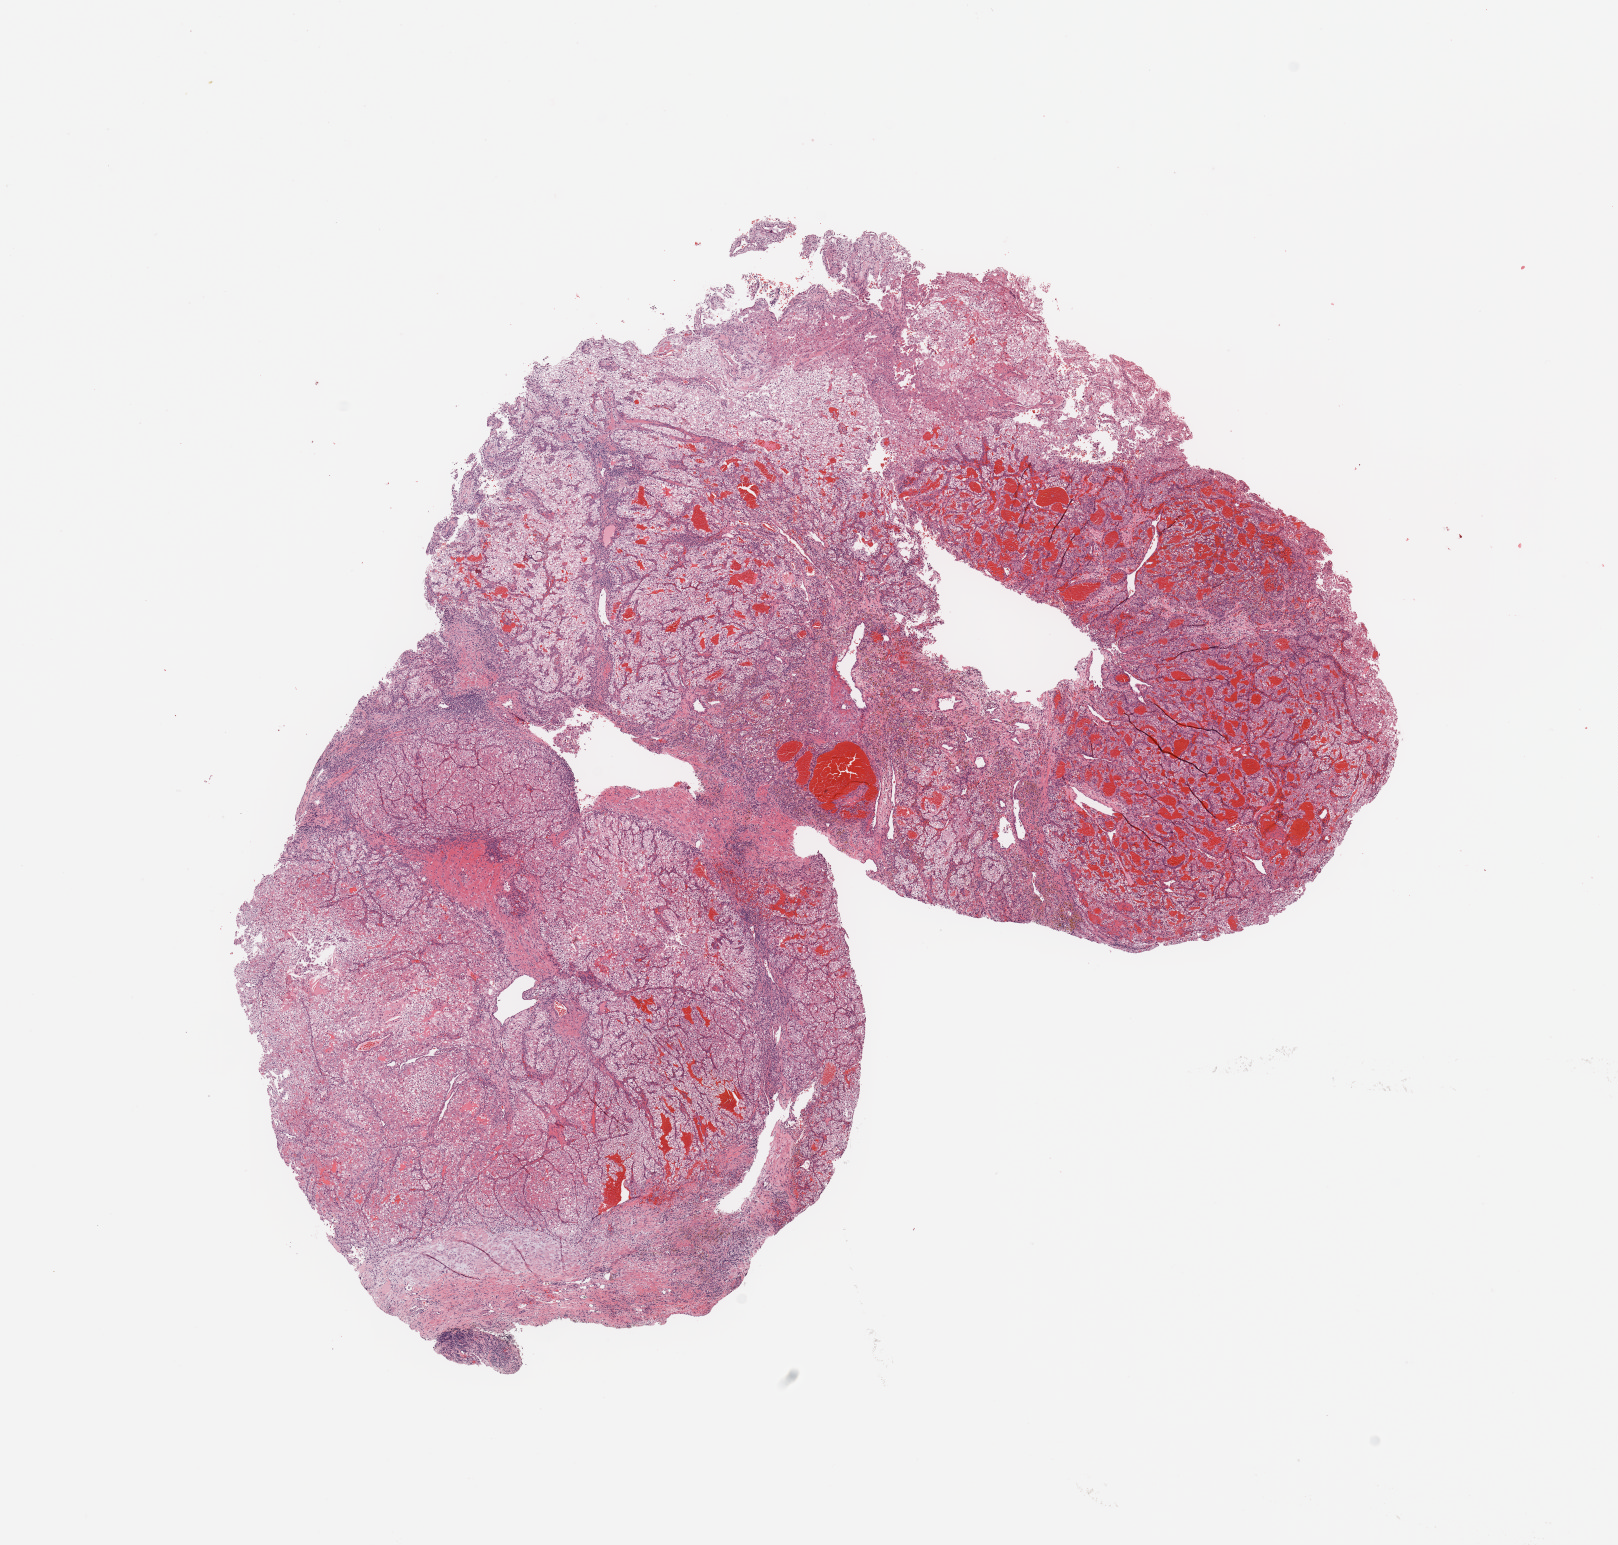
Whole-slide histology image, H&E — whole scanned area (about 12.8 x 12.2 mm, from a 20x scan) shown as a low-resolution overview; tumour tissue sample, sampled site: kidney. 53-year-old male patient. Histologic grade: G3 (poorly differentiated). Slide review estimates, as recorded: tumour nuclei 90%, necrosis 5%.
AJCC pathologic stage: I. Histologic diagnosis: Renal cell carcinoma, NOS. Primary tumour site (as recorded): upper pole.